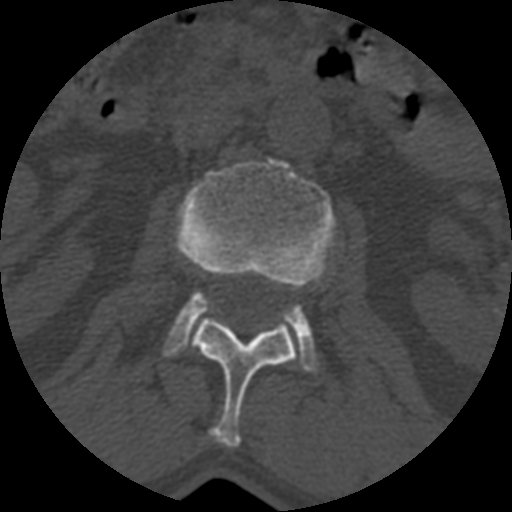
CT including the spine, one axial slice; 120 kVp; bone window (W 1800 / L 400 HU); 512 × 512 image matrix, field of view 160 × 160 mm. Patient age 71 years. From the clinical record (not read from this slice): primary cancer: prostate.
Outlined on this slice (semi-automatically segmented with operator editing):
- L1 vertebra: bounding box [x1, y1, x2, y2] px = [193, 317, 294, 447]
- L2 vertebra: [163, 158, 335, 376]